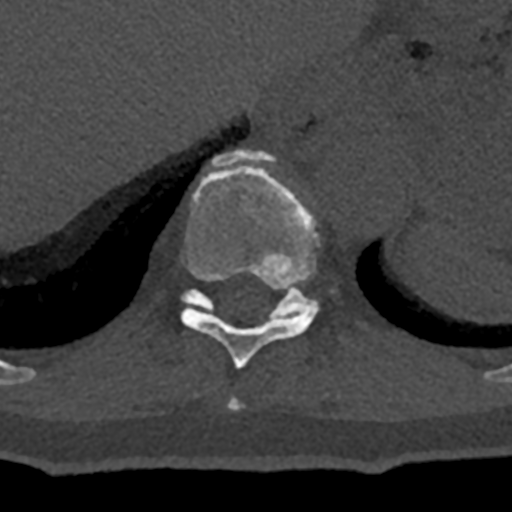
CT including the spine, one axial slice; position 590 of 797 along the scan axis; bone window (W 1800 / L 400 HU); 0.5 mm slice thickness; 512 × 512 image matrix. Patient: male, 74 years. Case-level facts recorded for this patient, not image findings: primary cancer: renal.
Structures marked on this image (semi-automatically segmented with operator editing):
- T10 vertebra: bounding box <181,150,320,369> (left, top, right, bottom; pixels)
- T11 vertebra: <182,282,317,319>
- T9 vertebra: <228,397,243,410>